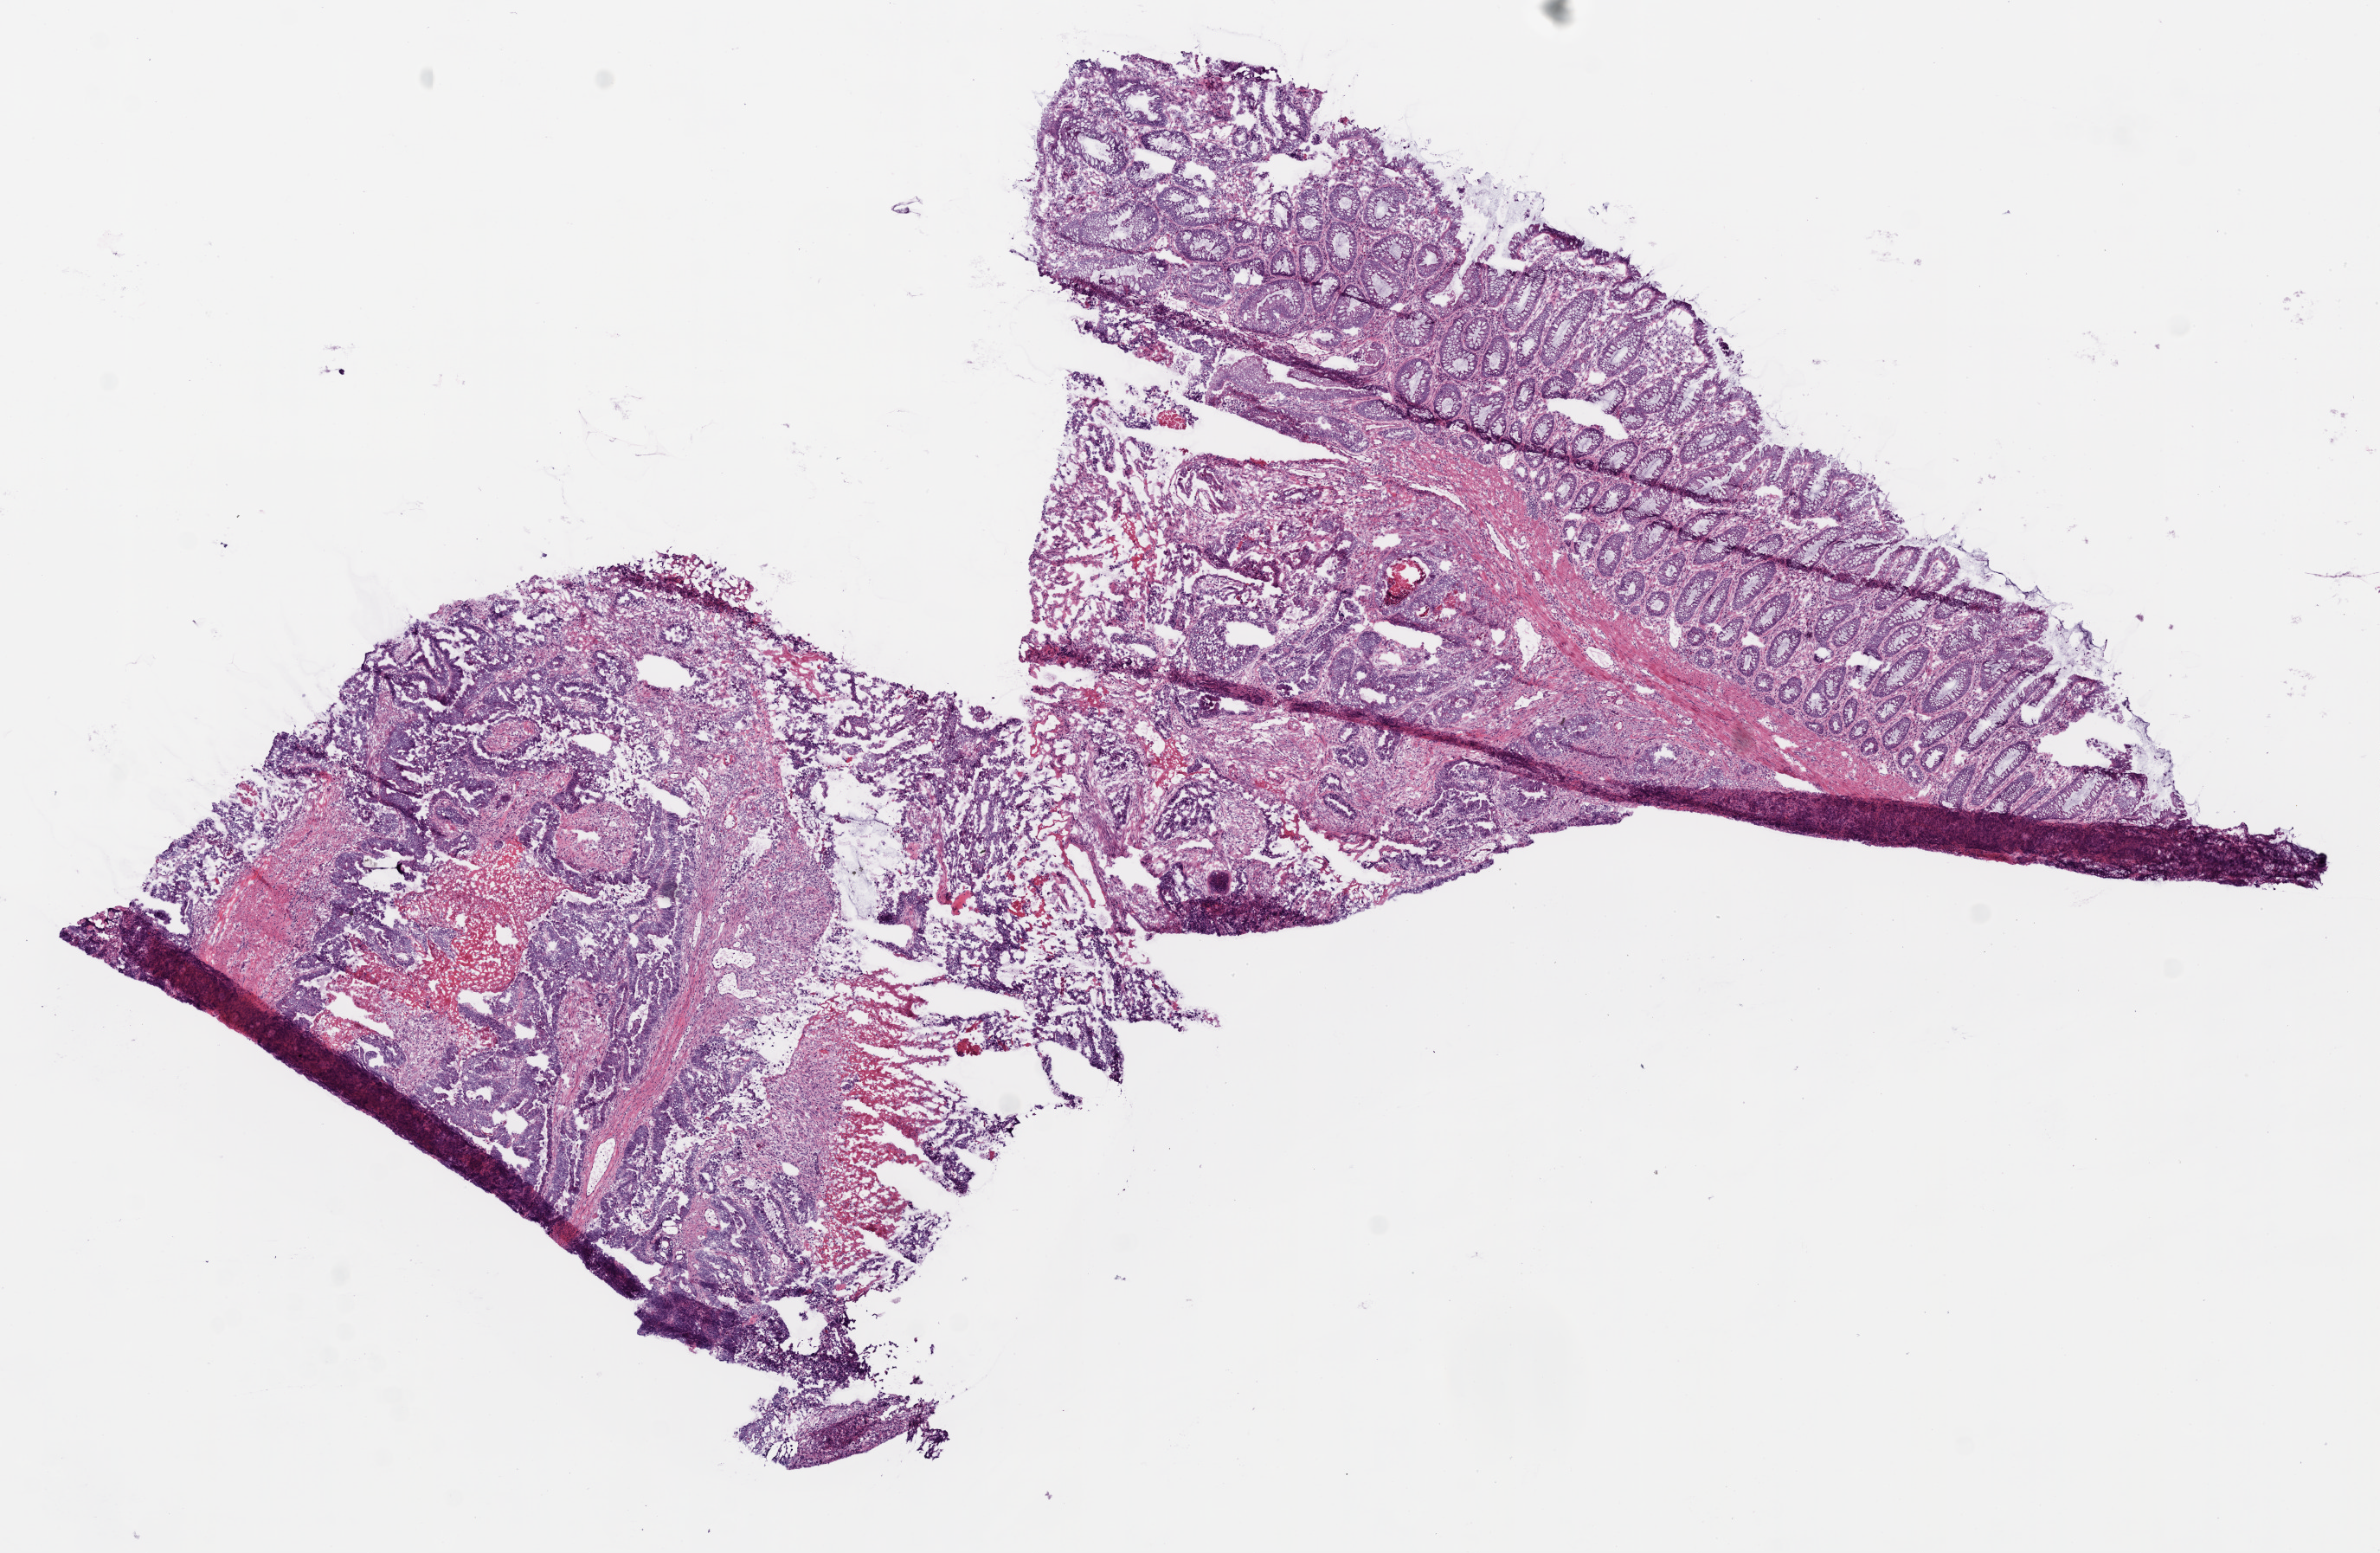
Whole-slide histology image, H&E-stained — whole scanned area (about 11.0 x 7.2 mm, slide scanned at 20x) shown as a low-resolution overview; frozen section; rectum, primary tumour sample. Patient: male, age at initial diagnosis 63 years. Pathologist review of this section (percent, as recorded): tumour cells 57%, tumour nuclei 65%, normal cells 30%, stromal cells 10%, necrosis 3%.
- pathologic diagnosis: Adenocarcinoma, NOS (colon, NOS)
- AJCC pathologic stage: IIA (6th edition)